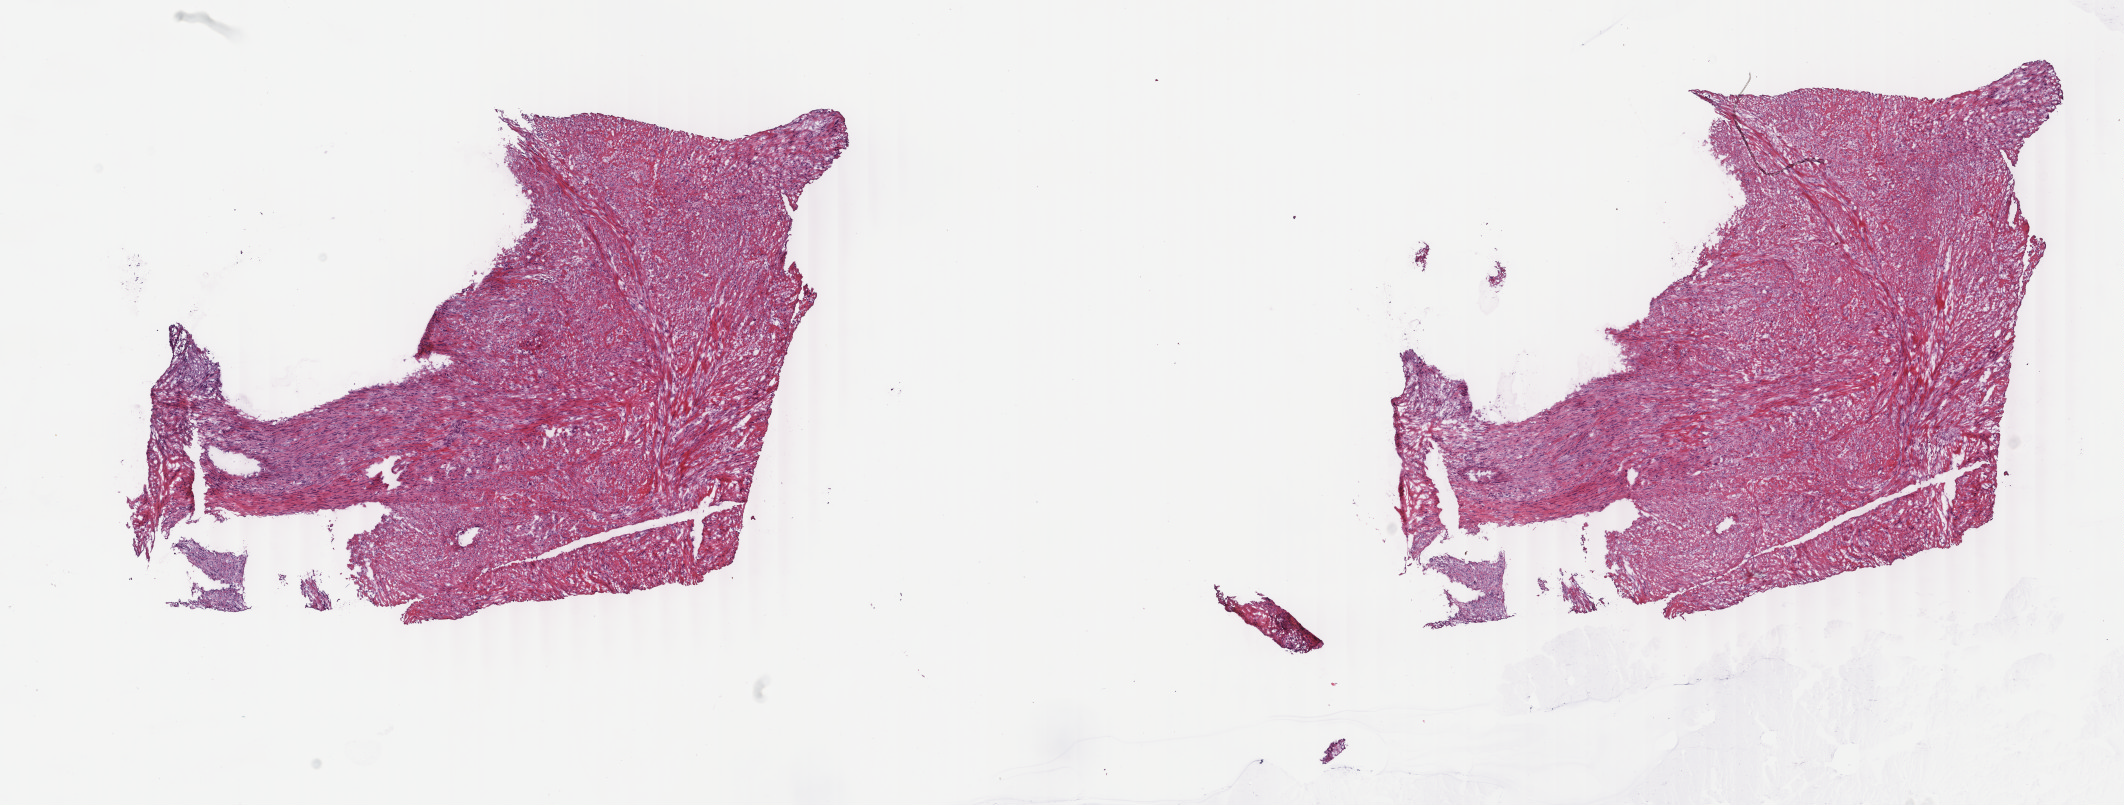
Digitized H&E-stained tissue section (whole slide), a low-resolution overview of the entire scanned area, about 16.9 x 6.4 mm; frozen section; sample: primary tumour, connective, subcutaneous and other soft tissues. Patient: male, age at initial diagnosis 81 years. Slide review estimates, as recorded: tumour cells 100%, tumour nuclei 95%, normal cells 0%, stromal cells 0%, necrosis 0%. Infiltration values recorded for this section: lymphocyte infiltration 0%, monocyte infiltration 0%, neutrophil infiltration 0%.
- diagnosis: Dedifferentiated liposarcoma